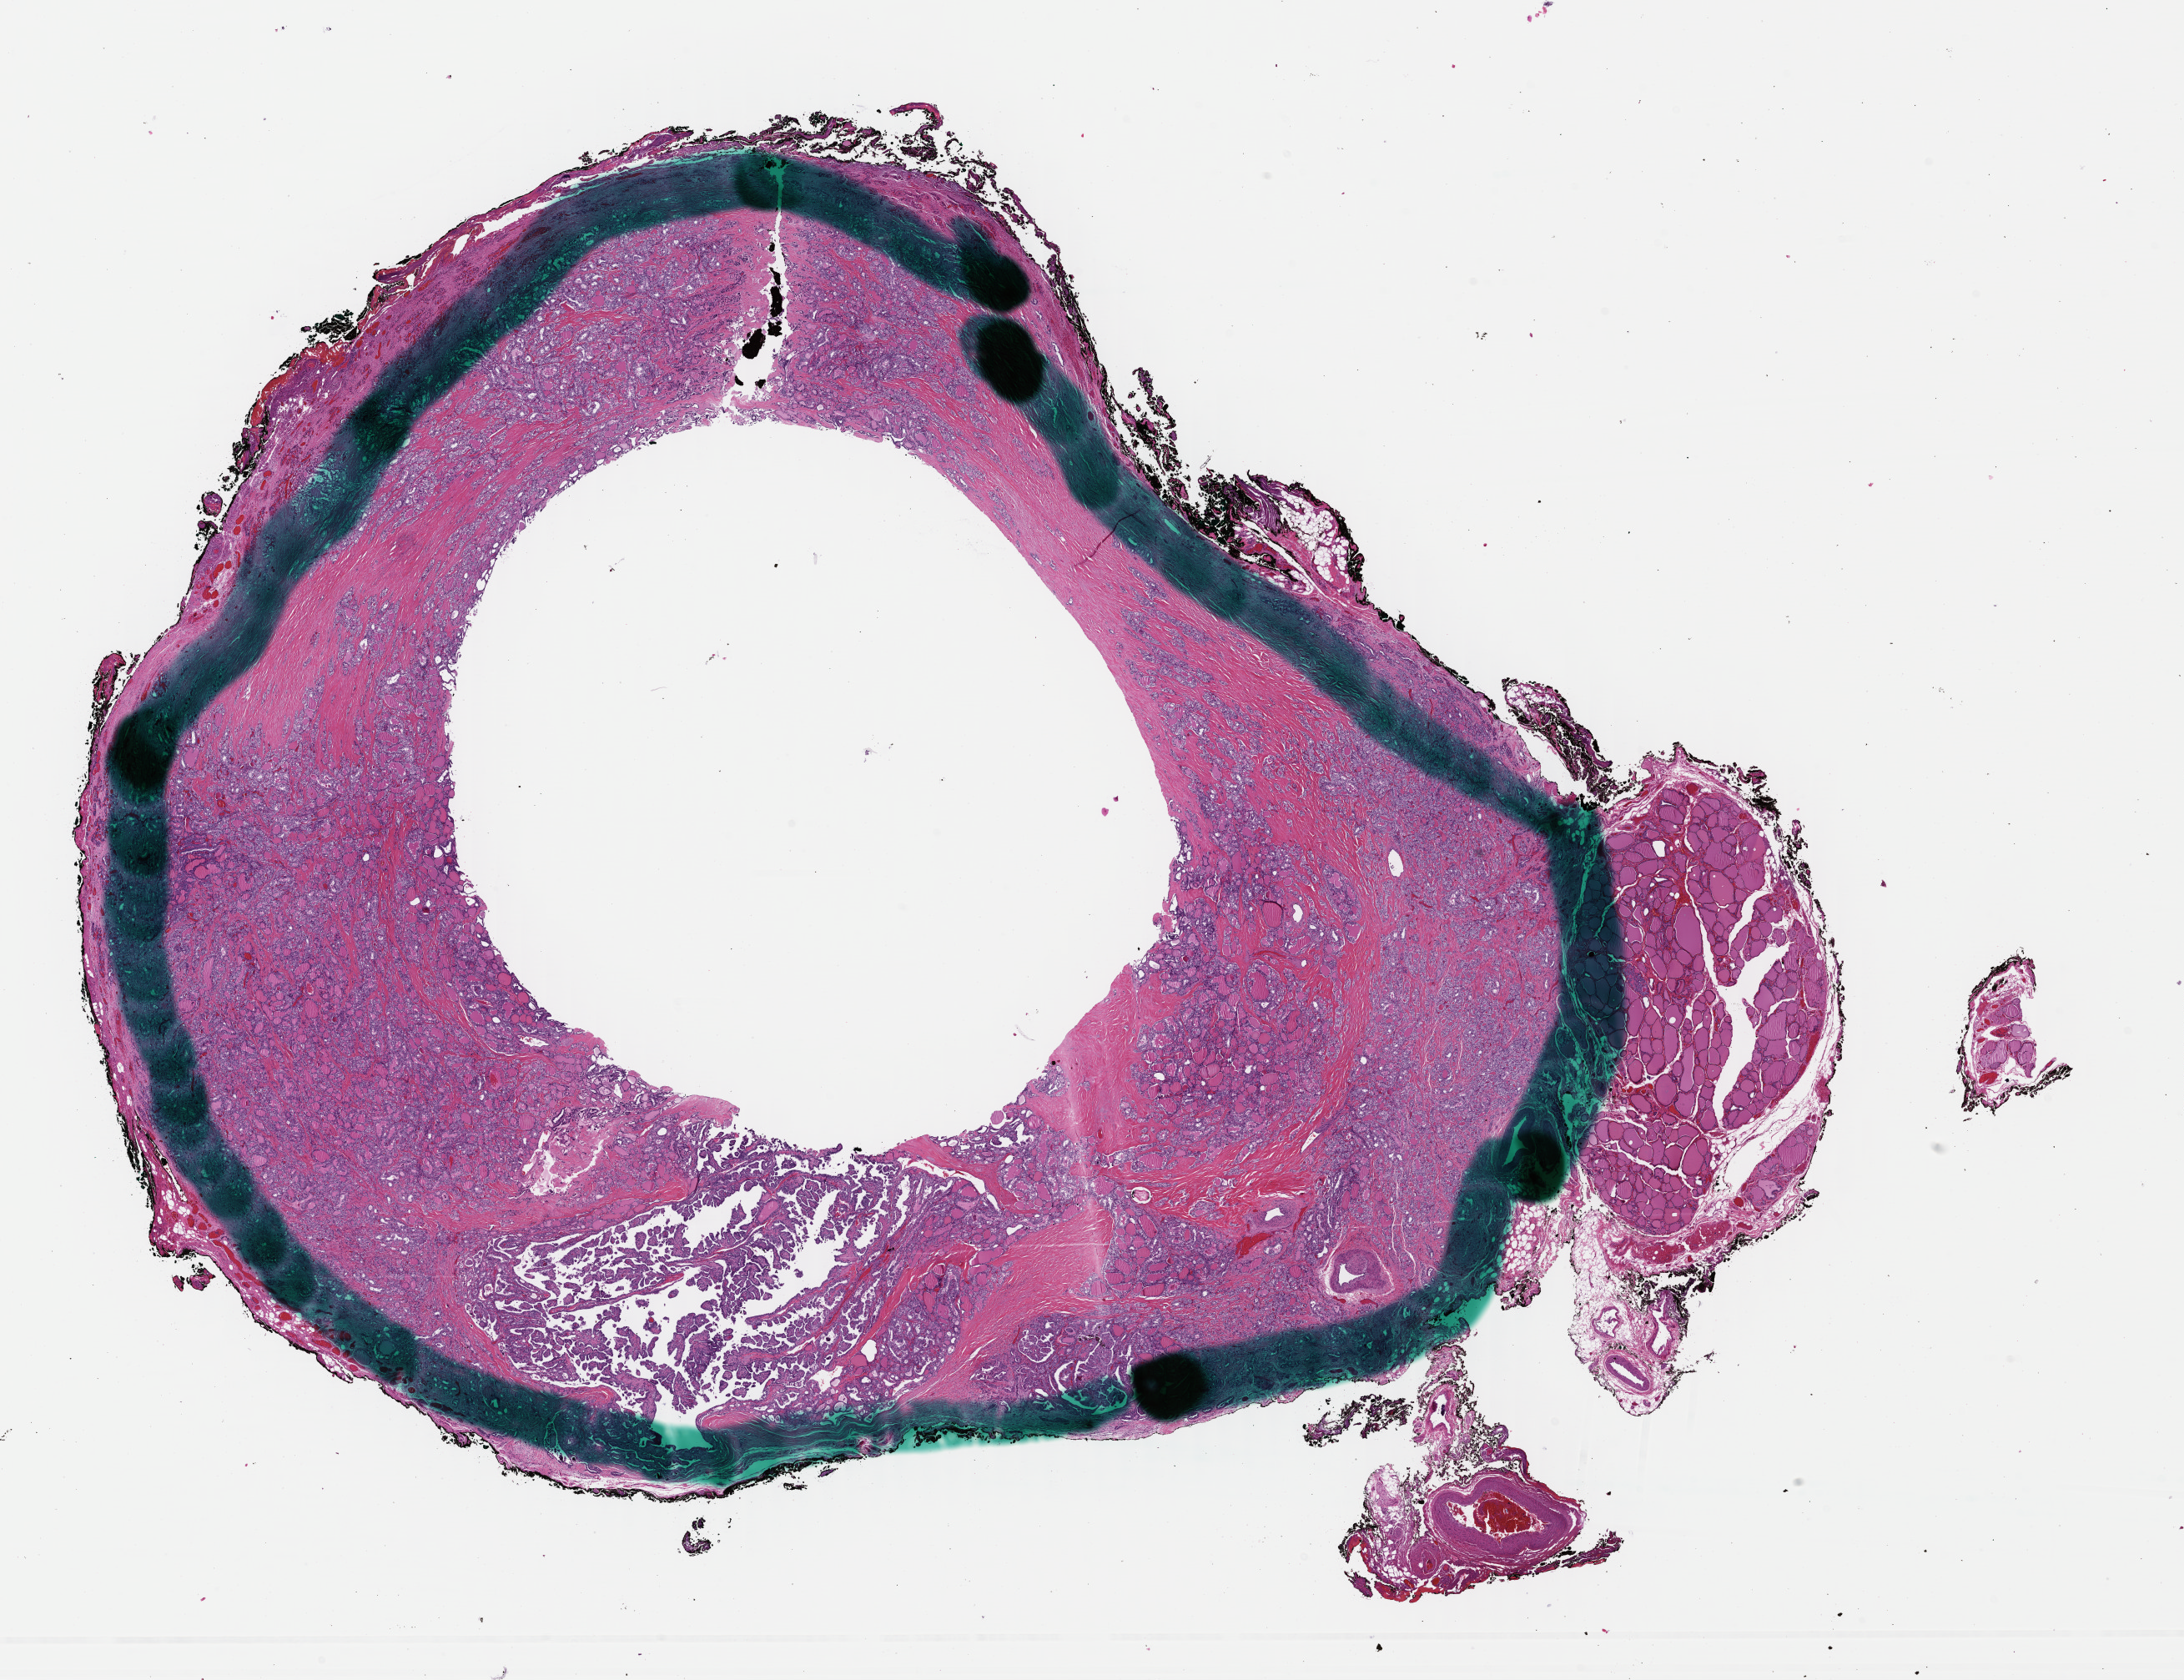
Whole-slide histology image, H&E — shown as a low-resolution overview of the whole scanned area (about 20.6 x 15.8 mm, from a 40x scan); FFPE section; thyroid, primary tumour sample. Male, age 51 years at initial diagnosis.
• TNM: T3 N1a MX
• AJCC pathologic stage: III (6th edition)
• laterality: right
• histologic diagnosis: Papillary adenocarcinoma, NOS
• lymph nodes positive (case pathology): 20 of 85 examined